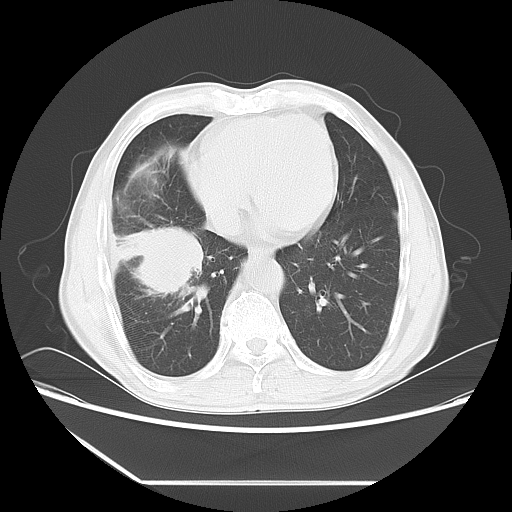
Chest CT, one axial slice. Position 22 of 60 along the scan axis. Reconstruction kernel LUNG. 120 kVp. Lung window (W 1500 / L -600 HU). 5 mm slice thickness. 512 × 512 image matrix, field of view 386 × 386 mm. Patient: male, 72 years. From the clinical record (not read from this slice): clinical TNM (as recorded): T1c N0 M0.
Structures marked on this image (bounding box drawn by a radiologist):
- lung tumour (recorded histology: squamous cell carcinoma): bounding box (x1, y1, x2, y2) in pixels: (117, 215, 201, 300)